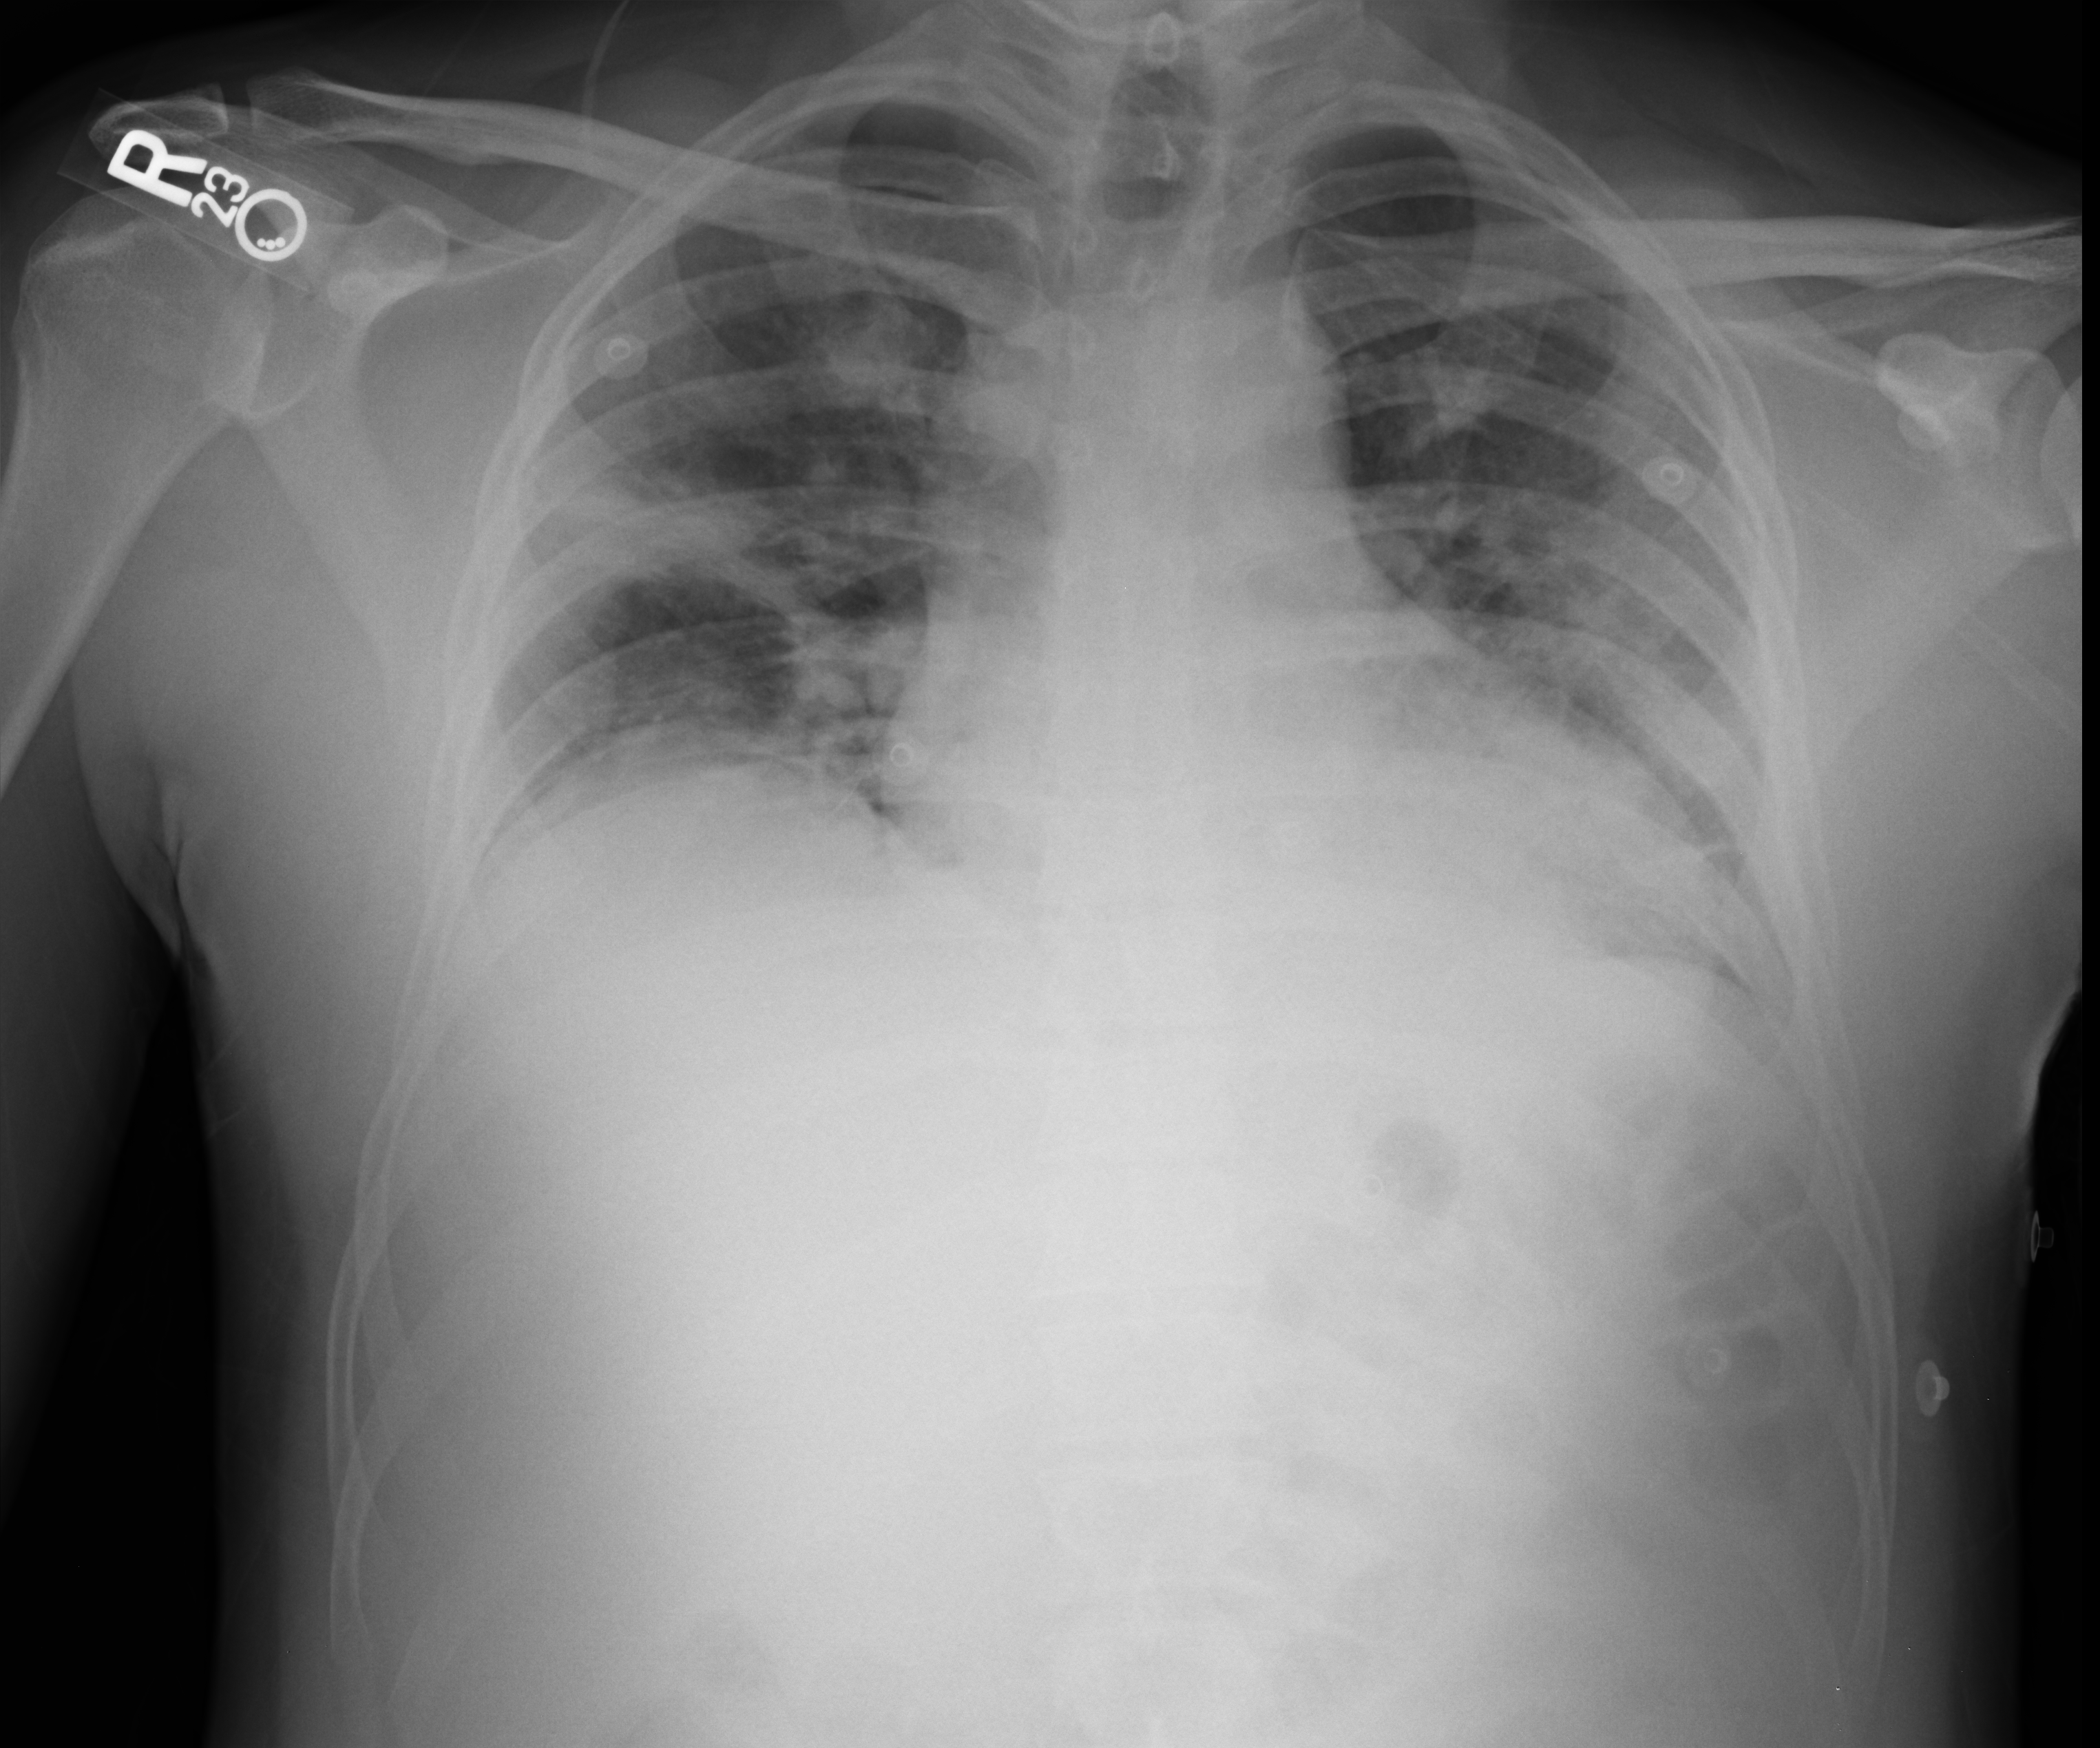
Chest X-ray (portable); anteroposterior (AP) projection. Patient hospitalised with COVID-19; male, aged 18–59 years.
Admission-level facts for this patient (not findings on this image; timing relative to this image not recorded):
- admitted to intensive care during this hospital stay: no
- other chronic lung disease (admission record): no
- COPD (admission record): no